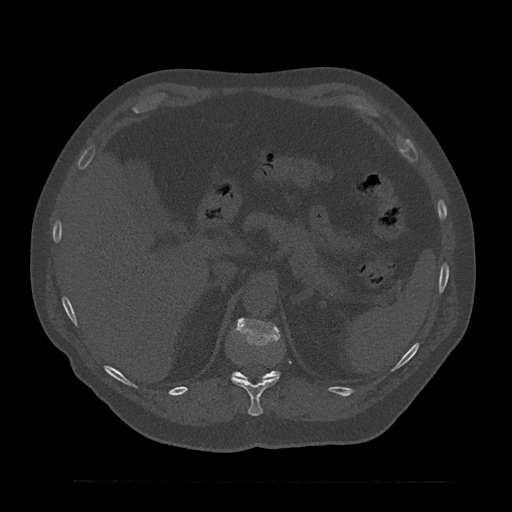
CT including the spine, one axial slice; position 267 of 797 along the scan axis; reconstruction kernel Br40s/3; bone window (W 1800 / L 400 HU); 0.5 mm slice thickness; 512 × 512 image matrix, field of view 430 × 430 mm. Patient: male, 61 years. Case-level facts recorded for this patient, not image findings: primary cancer: prostate.
Annotated regions visible in this slice (semi-automatically segmented with operator editing):
- L1 vertebra: bounding box (x1, y1, x2, y2) in pixels: (262, 379, 266, 380)
- T11 vertebra: (231, 375, 279, 416)
- T12 vertebra: (233, 318, 279, 380)